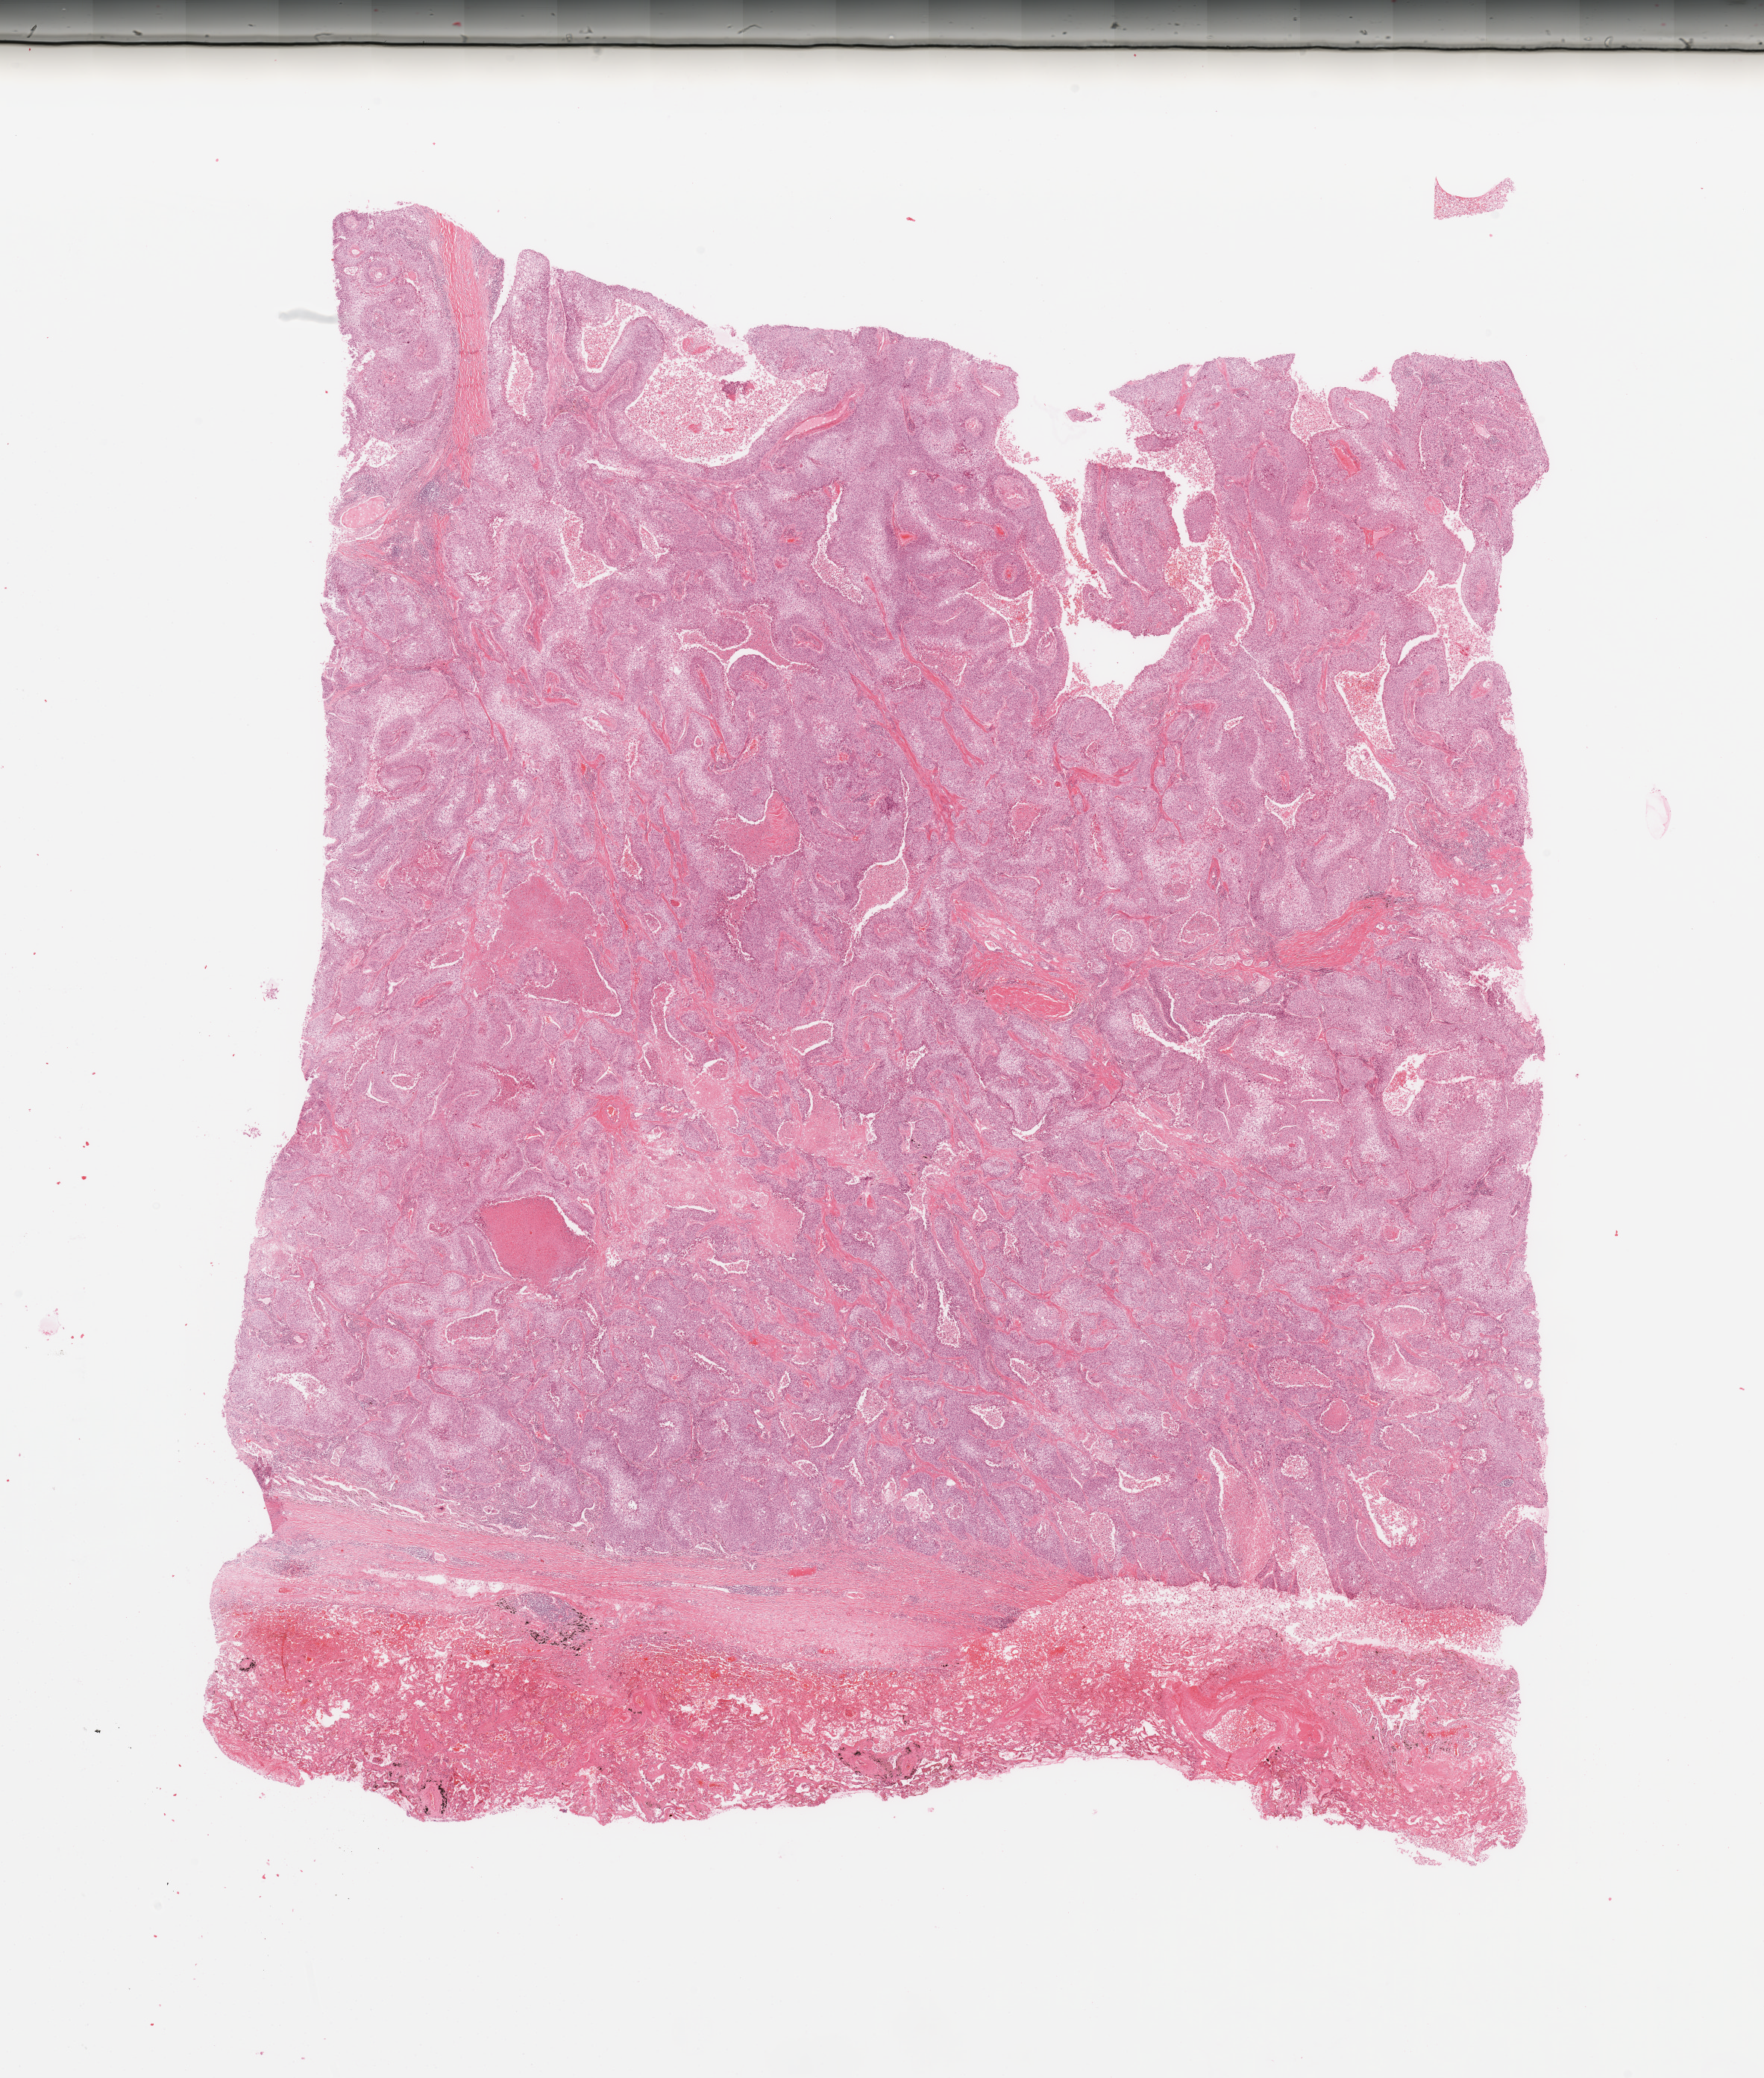
H&E-stained whole-slide image — low-resolution overview of the scanned area, about 18.7 x 22.0 mm (acquisition: 20x scan). Tumour tissue sample, sampled site: lung. Patient: male, age 59 years. Histologic grade: G2 (moderately differentiated). Slide review estimates, as recorded: tumour nuclei 85%, necrosis 5%.
* diagnosis: Squamous cell carcinoma, NOS
* AJCC pathologic stage: IIB